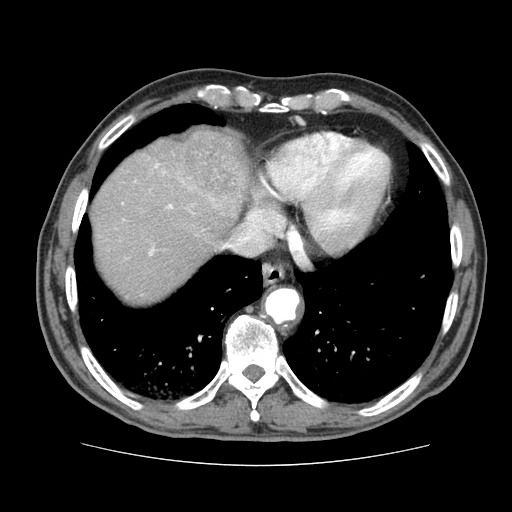
Contrast-enhanced abdominal CT (liver protocol), one axial slice; slice 69 of 79 in the series (ordered by position); reconstruction kernel STANDARD; soft-tissue window (W 400 / L 40 HU); 512 × 512 image matrix. From the clinical record (not read from this slice): diagnosis: hepatocellular carcinoma (patient treated with transarterial chemoembolisation; whether this scan precedes or follows treatment is not stated here); TNM stage (as recorded): Stage-I; Child-Pugh class: A; tumour nodularity: uninodular.
Structures marked on this image (semi-automatic segmentation, software-assisted and operator-edited):
- abdominal aorta: bounding box <267,290,300,321> (left, top, right, bottom; pixels)
- liver parenchyma outside the tumour (the mass and vessels are separate outlines, so this box may not span the whole liver): <92,131,246,302>
- mass: <153,127,256,217>
- liver vessels: <149,163,173,256>